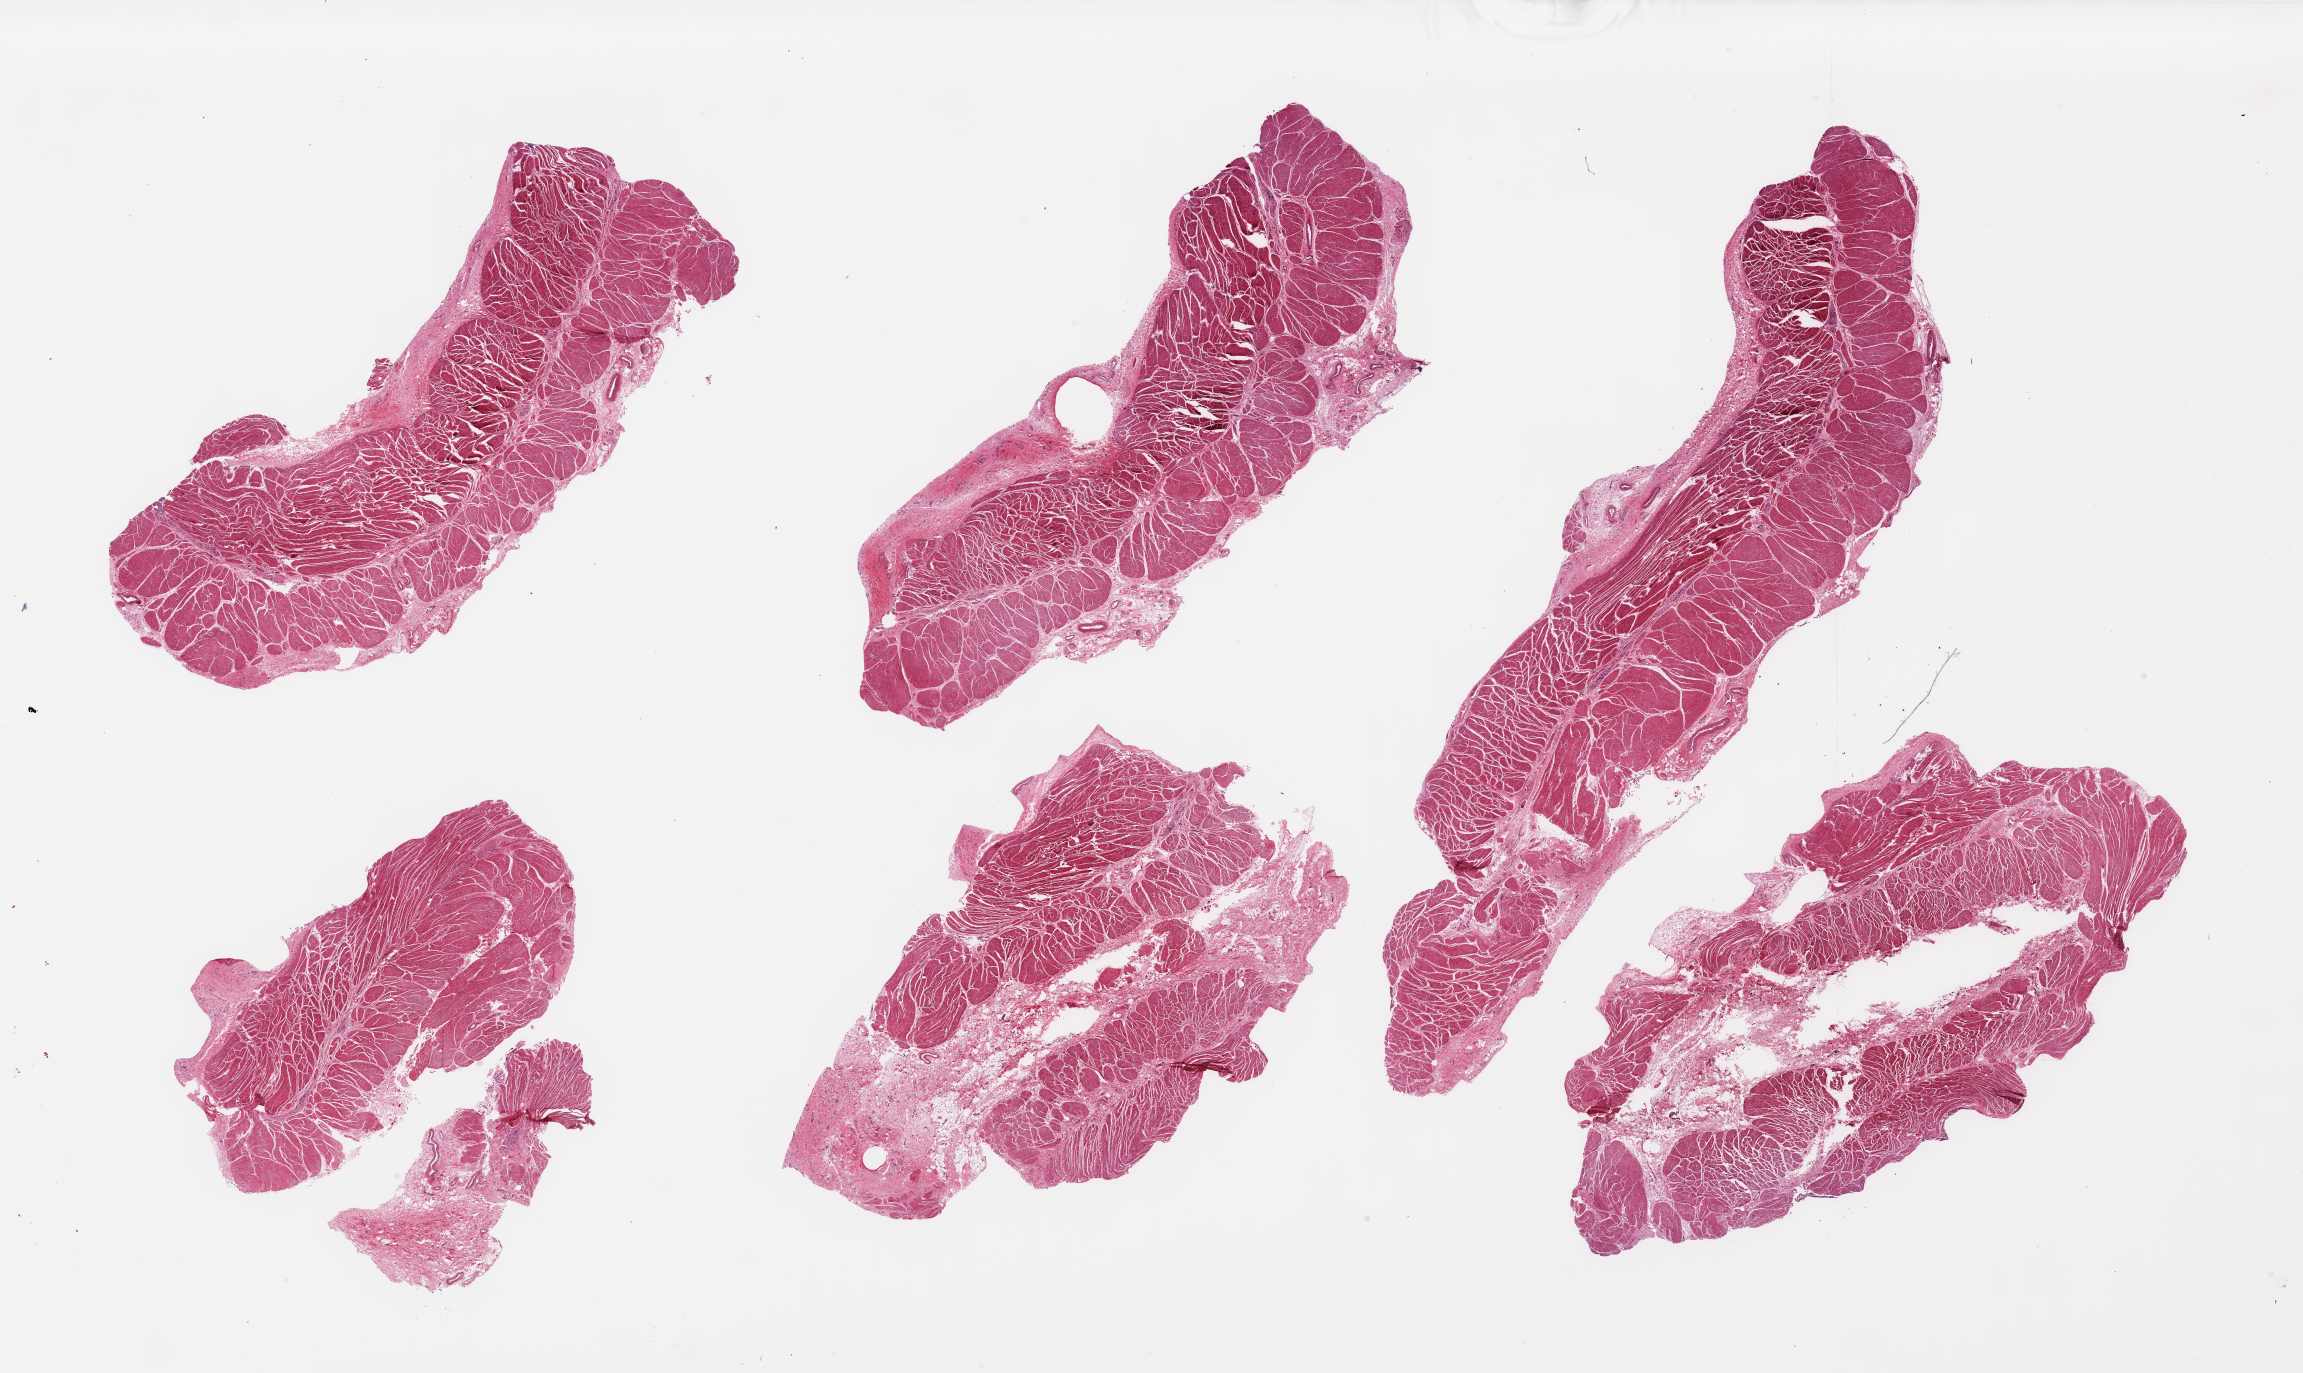
Digitized H&E-stained section, brightfield — shown as a low-resolution overview of the whole scanned area (about 36.4 x 21.7 mm, from a 20x scan). PAXgene-fixed paraffin-embedded (PFPE) section. Section of gastroesophageal junction (target tissue). Tissue donor sample. Male donor.
Review note (as recorded): 6 pieces; well dissected muscularis with variable amounts of fibrofatty stroma.